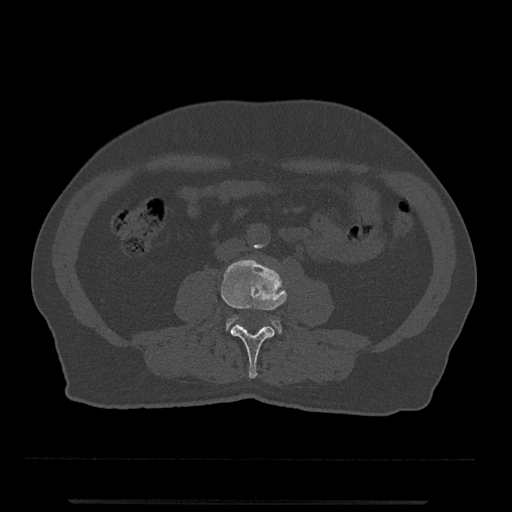
CT including the spine, one axial slice. Slice 184 of 797 in the series (ordered by position). 120 kVp. Bone window (W 1800 / L 400 HU). 0.5 mm slice thickness. 512 × 512 image matrix, field of view 419 × 419 mm. Patient: male, 63 years. Case-level facts recorded for this patient, not image findings: primary cancer: prostate.
Outlined on this slice (semi-automatically segmented with operator editing):
- L3 vertebra: bounding box (x1, y1, x2, y2) in pixels: (221, 259, 287, 379)
- L4 vertebra: (226, 317, 282, 334)